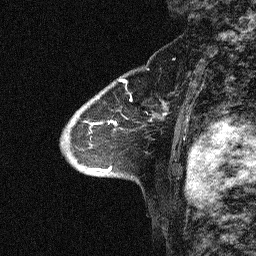
Breast MRI (dynamic contrast-enhanced), one sagittal slice; position 44 of 64 along the scan axis; dynamic contrast-enhanced study with each time point stored as its own series, time point 2 of 3 at this slice position (early post-contrast, ordered by acquisition time); 1.5 T; TE 4.5 ms, TR 11 ms; 2.06 mm slice thickness; 256 × 256 image matrix. Patient: female, 46 years. From the clinical record (not read from this slice): setting: breast cancer imaged before/during neoadjuvant chemotherapy; receptor status: HER2-positive.
Outlined on this slice (semi-automatically segmented with operator editing):
- analysis volume of interest (the breast-tissue region the enhancement analysis was run in; not a lesion): bounding box <46,51,180,169> (left, top, right, bottom; pixels)
- tumour enhancement mask (voxels above the 90 % enhancement threshold inside the analysis volume of interest): <149,114,164,121>